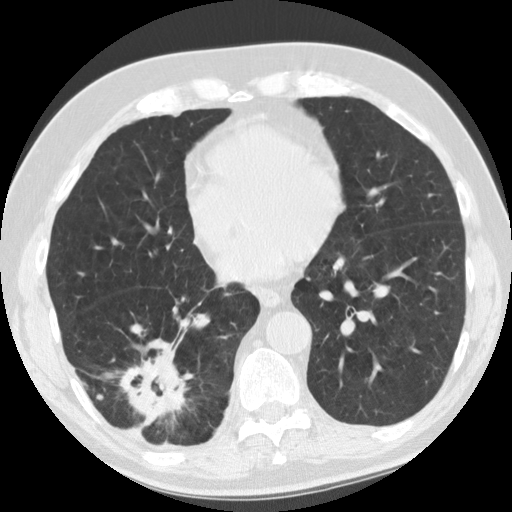
Low-dose screening chest CT, one axial slice. Slice 47 of 135 in the series (ordered by position). Reconstruction kernel STANDARD. Lung window (W 1500 / L -600 HU). 2.5 mm slice thickness. 512 × 512 image matrix, field of view 340 × 340 mm.
Outlined on this slice (outlined manually by an expert reader):
- lesion 1 (tumor, lower lobe of right lung): box from (x=115, y=338) to (x=193, y=424) px